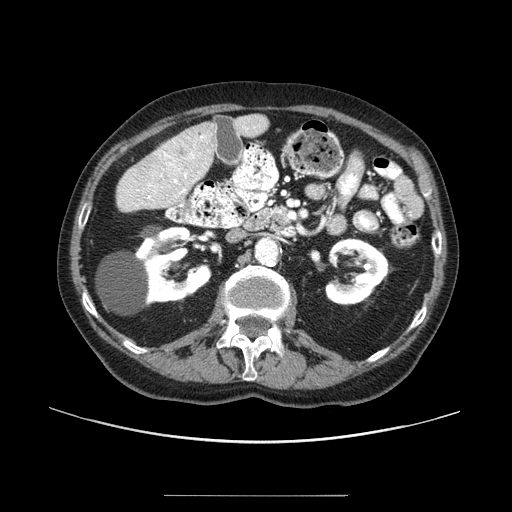
Contrast-enhanced abdominal CT (liver protocol), one axial slice; slice 34 of 91 in the series (ordered by position); 100 kVp; one of 2 acquisitions stored at this slice position; soft-tissue window (W 400 / L 40 HU); 2.5 mm slice thickness; 512 × 512 image matrix, field of view 400 × 400 mm. Case-level facts recorded for this patient, not image findings: diagnosis: hepatocellular carcinoma (patient treated with transarterial chemoembolisation; whether this scan precedes or follows treatment is not stated here); TNM stage (as recorded): Stage-I; Child-Pugh class: A; tumour nodularity: uninodular.
Structures marked on this image (semi-automatically segmented with operator editing):
- liver parenchyma outside the tumour (the mass and vessels are separate outlines, so this box may not span the whole liver): box from (x=148, y=122) to (x=218, y=200) px
- mass: (x=154, y=138)–(x=189, y=173)
- liver vessels: (x=171, y=134)–(x=207, y=198)